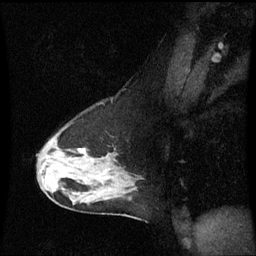
Breast MRI (dynamic contrast-enhanced), one sagittal slice; slice 40 of 60 in the series (ordered by position); dynamic contrast-enhanced series, image 2 of 3 at this slice position (ordered by acquisition); 1.5 T; TE 4.2 ms, TR 8.9 ms; 2 mm slice thickness; 256 × 256 image matrix, field of view 210 × 210 mm. Patient: female, 50 years. Case-level facts recorded for this patient, not image findings: setting: breast cancer imaged before/during neoadjuvant chemotherapy; receptor status: HR-positive, HER2-negative.
Structures marked on this image (semi-automatic segmentation, software-assisted and operator-edited):
- analysis volume of interest (the breast-tissue region the enhancement analysis was run in; not a lesion): bounding box (x1, y1, x2, y2) in pixels: (36, 130, 144, 210)
- tumour enhancement mask (voxels above the 70 % enhancement threshold inside the analysis volume of interest): (80, 150, 86, 153)